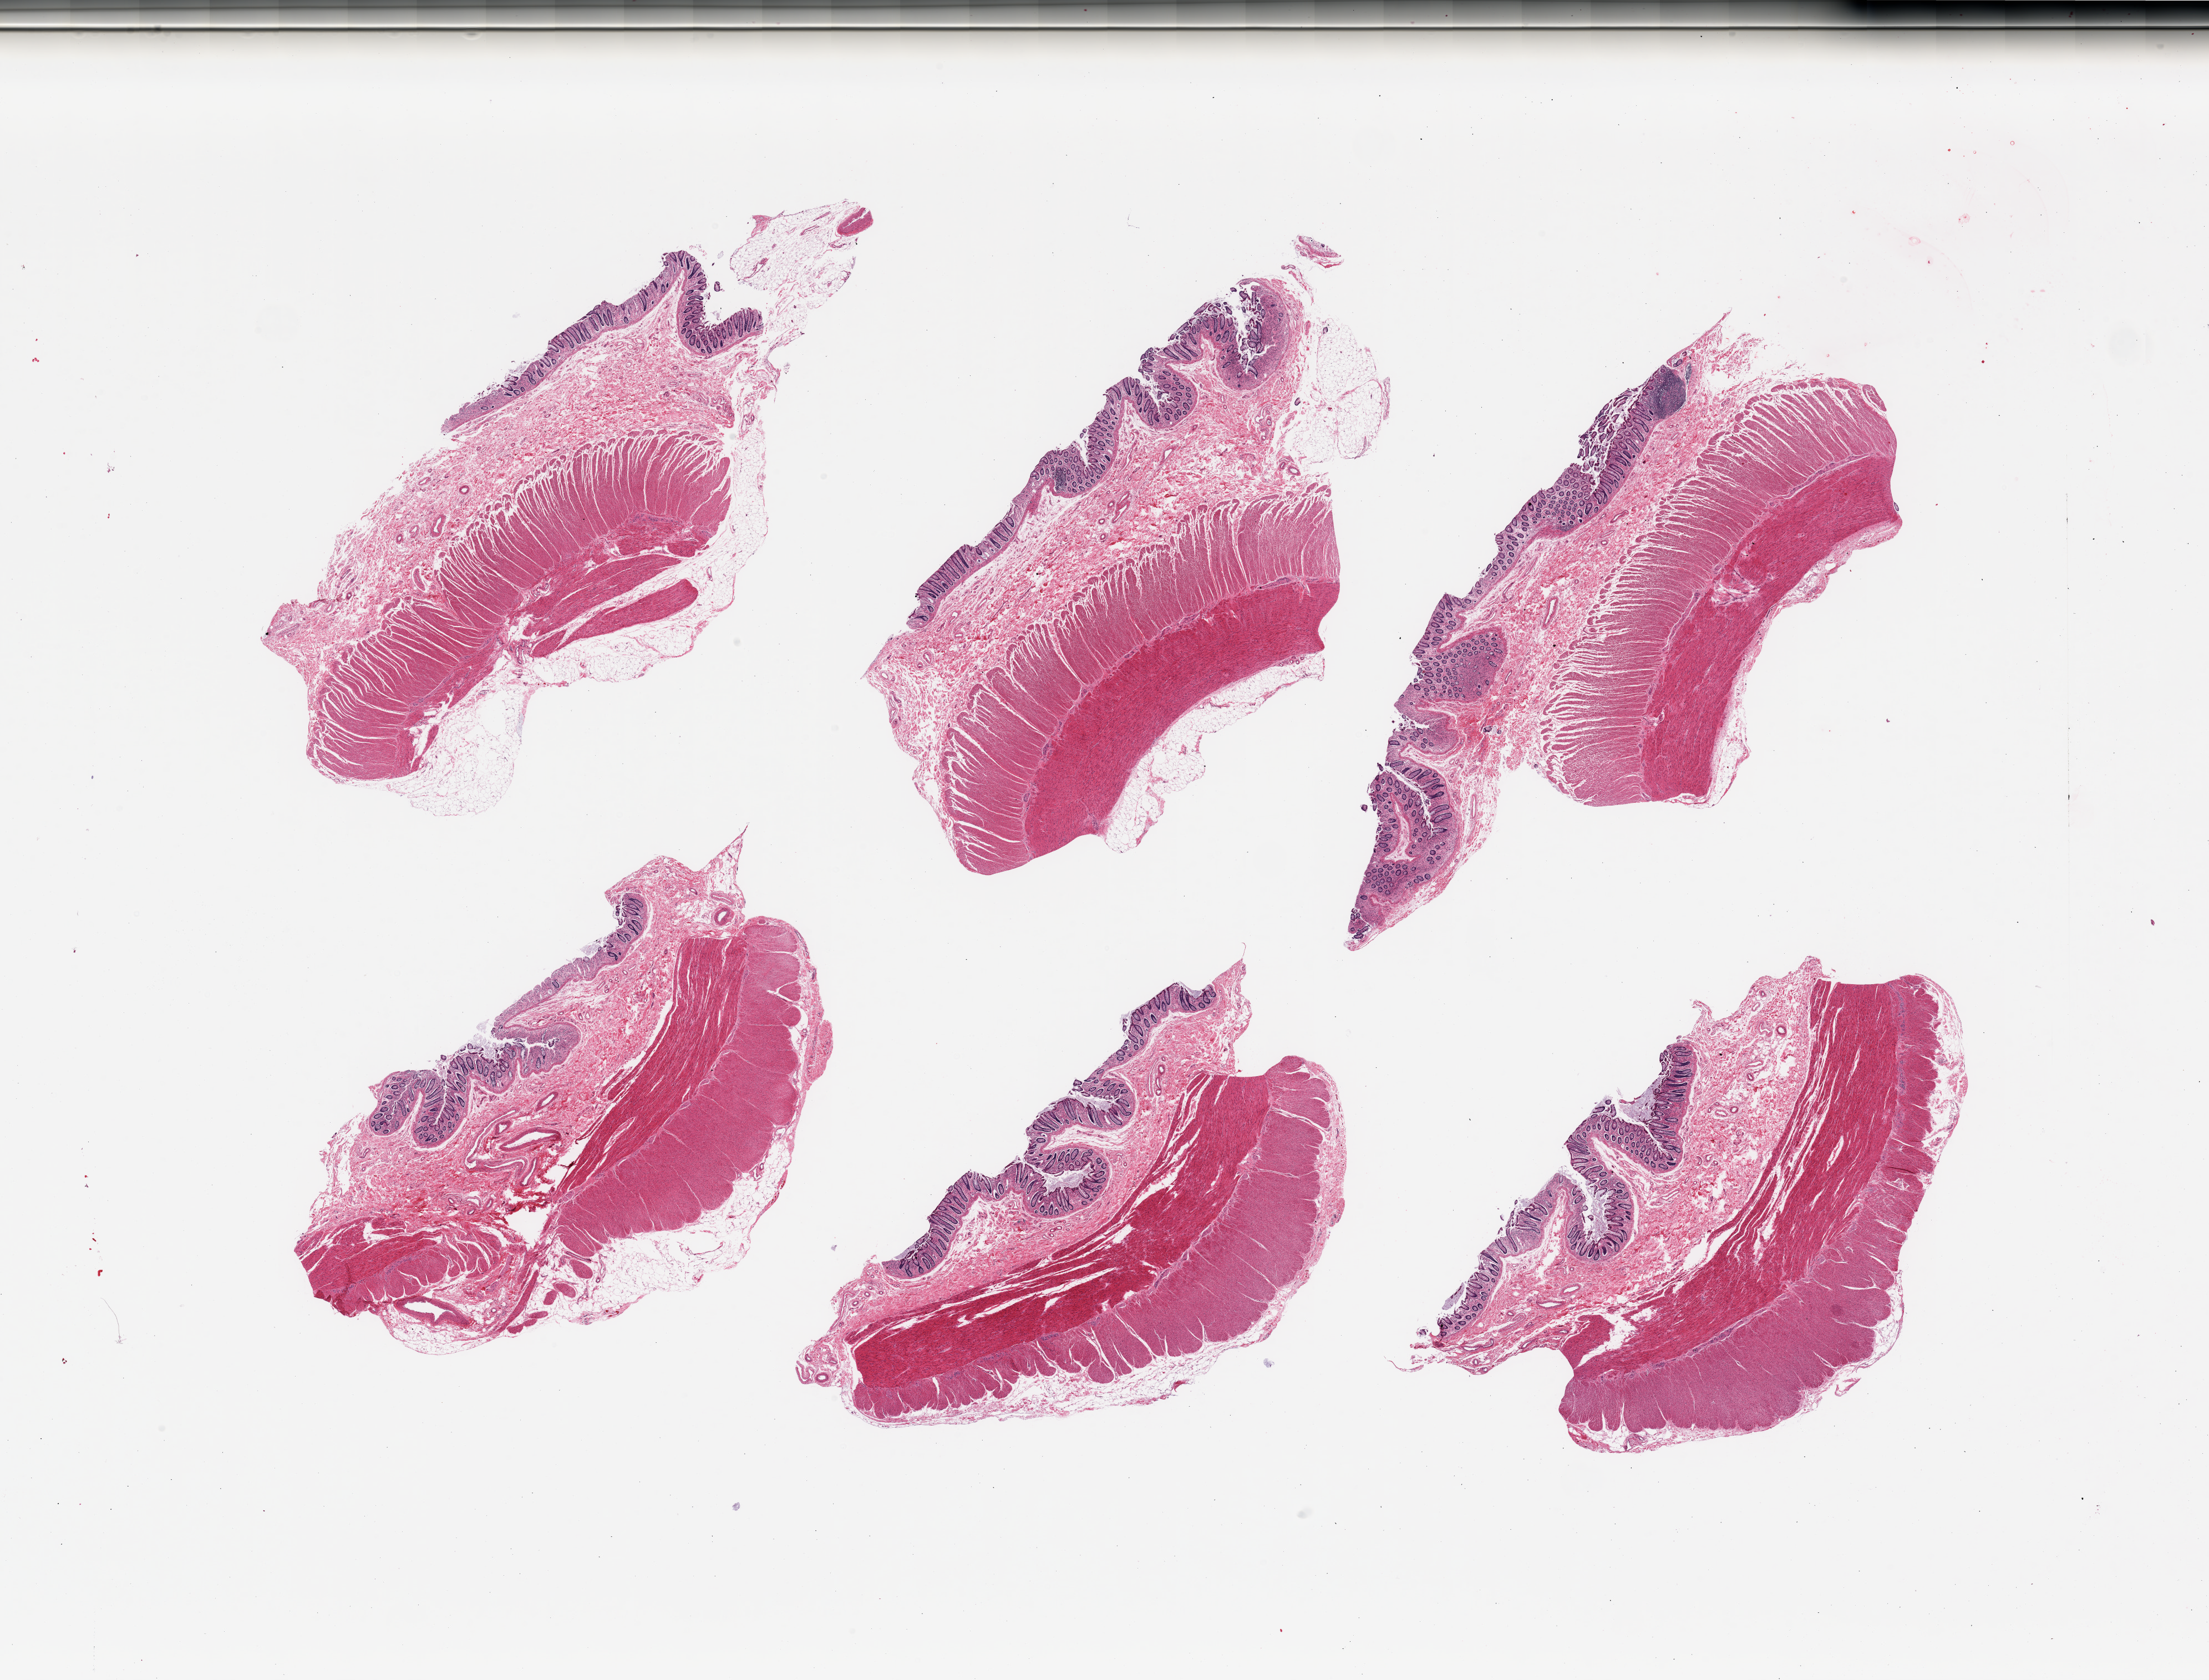
Hematoxylin and eosin (H&E) whole-slide image — whole scanned area (about 31.5 x 24.0 mm) shown as a low-resolution overview. PAXgene-fixed paraffin-embedded (PFPE) section. Sampled site (target tissue): transverse colon. Donor tissue sample. Donor: female.
Pathologist's review note for this sample: 6 pieces, target mucosa up to ~0.5mm, ~10% of thickness.